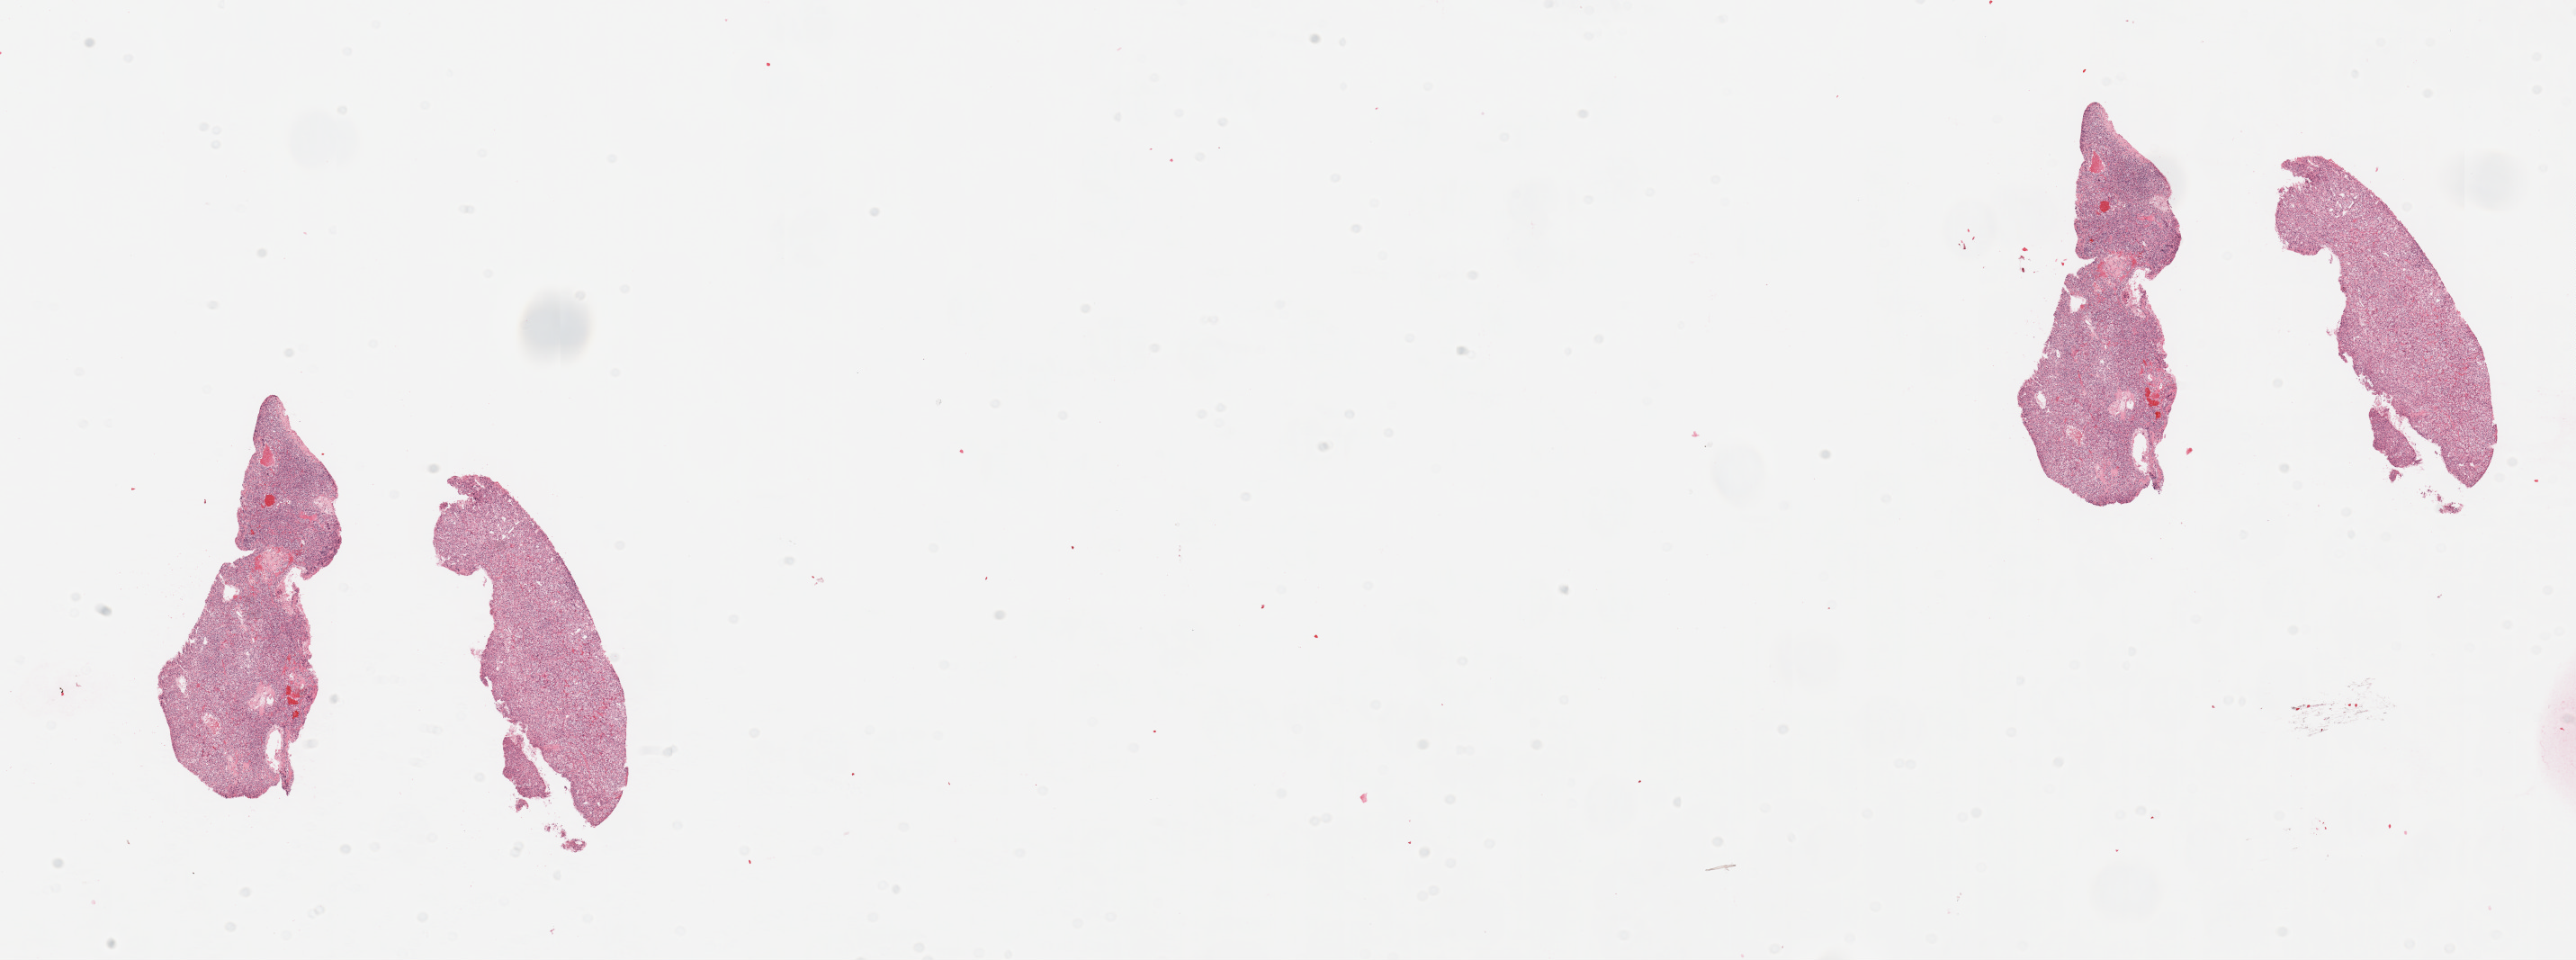
Whole-slide histology image, H&E — shown as a low-resolution overview of the whole scanned area (about 22.6 x 8.4 mm, slide scanned at 20x). Tumour tissue sample, sampled site: kidney. Patient: male, age 46 years. Histologic grade: G2 (moderately differentiated). Slide review estimates, as recorded: tumour nuclei 95%, necrosis 0%.
AJCC pathologic stage: I. Diagnosis: Renal cell carcinoma, NOS.